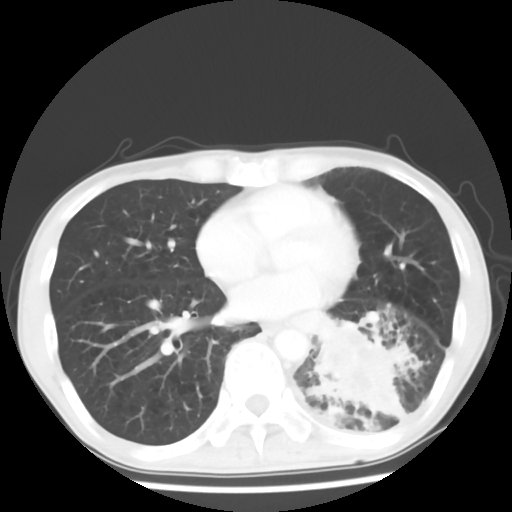
Chest CT, one axial slice. Reconstruction kernel STANDARD. 120 kVp. Lung window (W 1500 / L -600 HU). 5 mm slice thickness. 512 × 512 image matrix, field of view 313 × 313 mm. Patient: male, 68 years. Case-level facts recorded for this patient, not image findings: clinical TNM (as recorded): T4 N0 M0.
Annotated regions visible in this slice (bounding box drawn by a radiologist):
- lung tumour (recorded histology: squamous cell carcinoma): bounding box (x1, y1, x2, y2) in pixels: (302, 303, 395, 417)